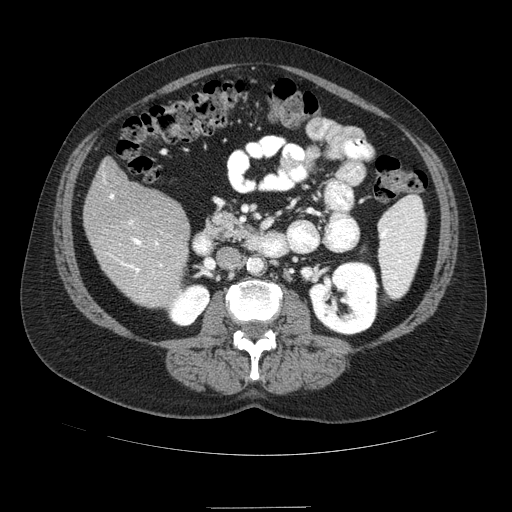
Contrast-enhanced abdominal CT (liver protocol), one axial slice; position 28 of 89 along the scan axis; 120 kVp; soft-tissue window (W 400 / L 40 HU); 2.5 mm slice thickness; 512 × 512 image matrix, field of view 400 × 400 mm. From the clinical record (not read from this slice): diagnosis: hepatocellular carcinoma (patient treated with transarterial chemoembolisation; whether this scan precedes or follows treatment is not stated here); TNM stage (as recorded): Stage-IIIB; Child-Pugh class: A; tumour nodularity: multinodular.
Annotated regions visible in this slice (semi-automatically segmented with operator editing):
- liver parenchyma outside the tumour (the mass and vessels are separate outlines, so this box may not span the whole liver): bounding box [x1, y1, x2, y2] px = [84, 158, 190, 306]
- liver vessels: [107, 194, 162, 273]